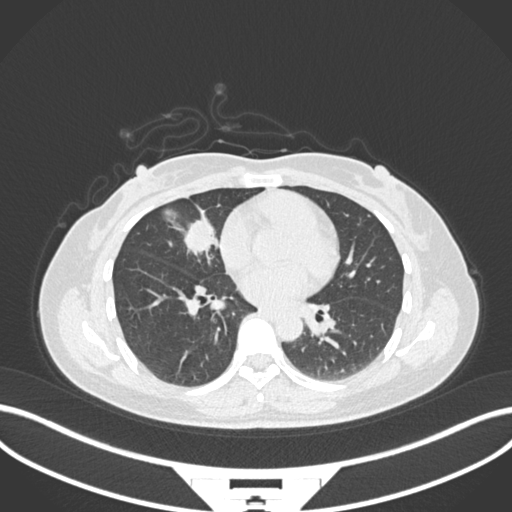
Chest CT, one axial slice. Slice 76 of 171 in the series (ordered by position). Reconstruction kernel B30f. 120 kVp. Lung window (W 1500 / L -600 HU). 512 × 512 image matrix, field of view 400 × 400 mm. Patient: female, 43 years. From the clinical record (not read from this slice): clinical TNM (as recorded): T1c N3 M1; histopathological grade: G1.
Structures marked on this image (bounding box drawn by a radiologist):
- lung tumour (recorded histology: adenocarcinoma): box from (x=179, y=211) to (x=221, y=263) px